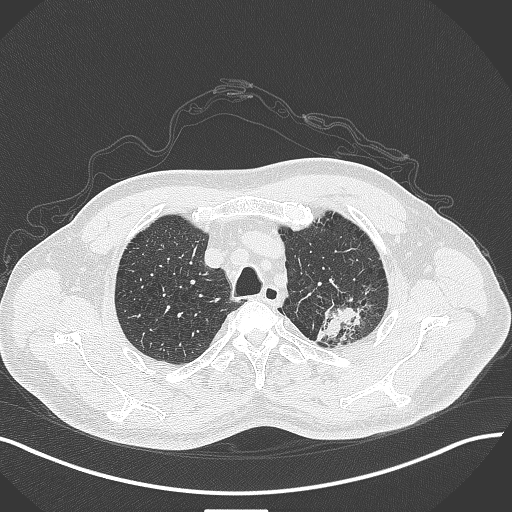
Chest CT, one axial slice; position 351 of 429 along the scan axis; reconstruction kernel B70f; lung window (W 1500 / L -600 HU); 1 mm slice thickness; 512 × 512 image matrix, field of view 400 × 400 mm. Male patient, age 55 years. Case-level facts recorded for this patient, not image findings: clinical TNM (as recorded): T3 N0 M1c; histopathological grade: G3.
Structures marked on this image (rectangle marked by the reading radiologist):
- lung tumour (recorded histology: adenocarcinoma): bounding box [x1, y1, x2, y2] px = [310, 291, 368, 346]